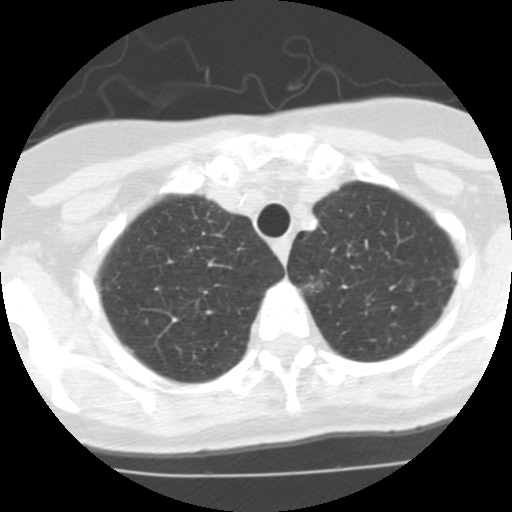
Low-dose screening chest CT, one axial slice; slice 98 of 113 in the series (ordered by position); 120 kVp; lung window (W 1500 / L -600 HU); 512 × 512 image matrix.
Outlined on this slice (outlined manually by an expert reader):
- lesion 1 (tumor, upper lobe of left lung): box from (x=452, y=268) to (x=461, y=281) px